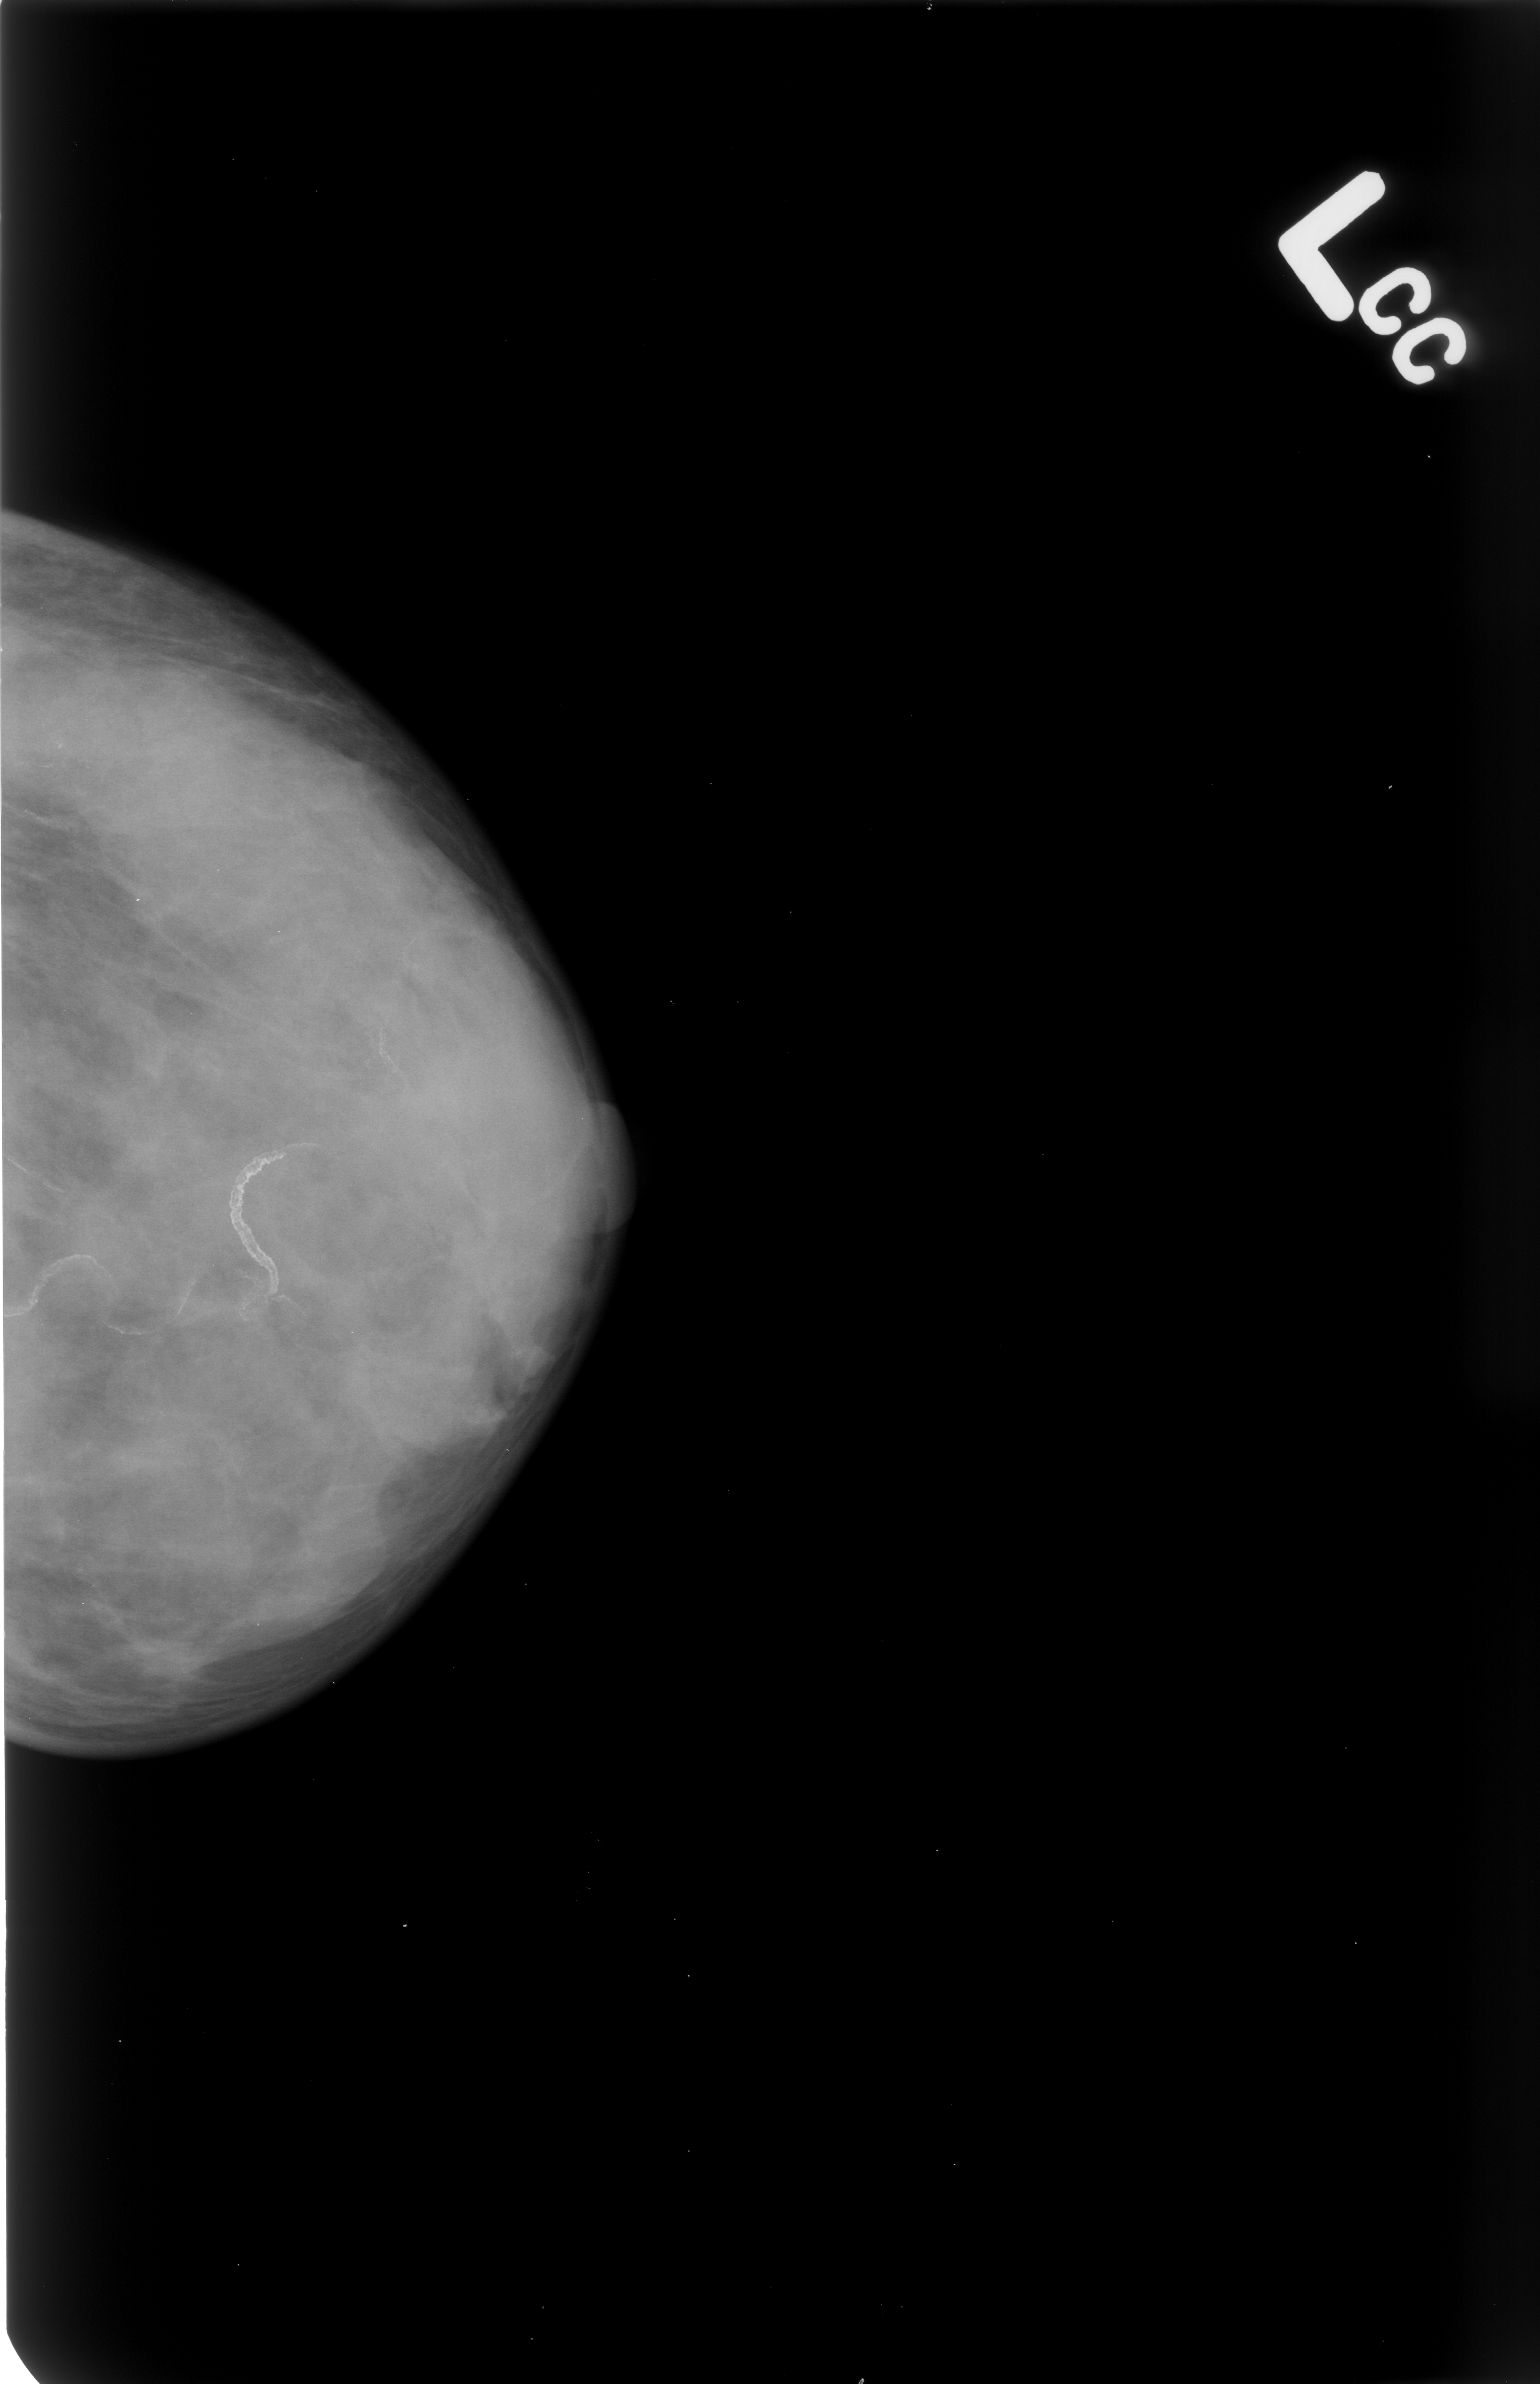
Scanned film-screen mammogram; left breast; CC view.
Marked findings (only marked abnormalities are described; nothing is implied about the rest of the image): calcifications, morphology vascular; BI-RADS assessment category 2; benign without callback (not worked up further).